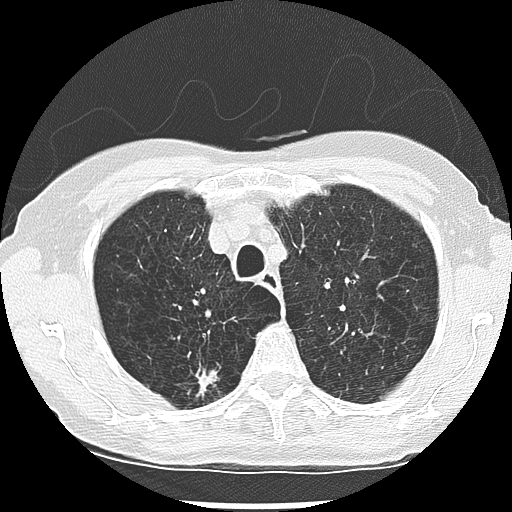
Low-dose screening chest CT, one axial slice; slice 217 of 265 in the series (ordered by position); lung window (W 1500 / L -600 HU); 512 × 512 image matrix.
Structures marked on this image (expert manual segmentation):
- lesion 1 (nodule, upper lobe of right lung): bounding box <197,371,217,397> (left, top, right, bottom; pixels)